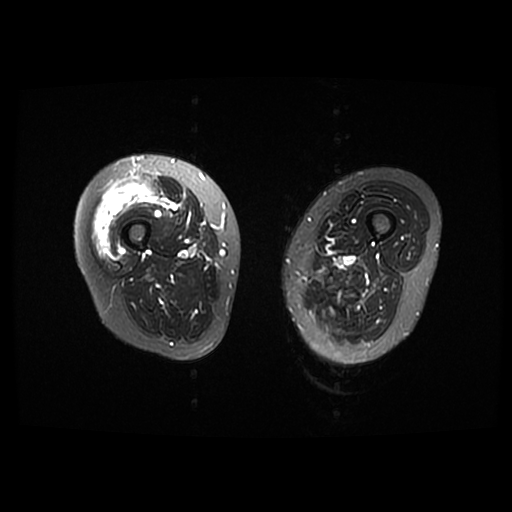
MRI of an extremity soft-tissue mass, one axial slice. Slice 9 of 42 in the series (ordered by position). T2-weighted fat-saturated. 6 mm slice thickness. 512 × 512 image matrix, field of view 440 × 440 mm. Female patient. Case-level facts recorded for this patient, not image findings: histological type: pleiomorphic undifferentiated sarcoma; grade: high; site of the primary tumour: right quadricep.
Outlined on this slice (expert manual segmentation):
- gross tumour volume including surrounding oedema: bounding box [x1, y1, x2, y2] px = [92, 183, 160, 258]